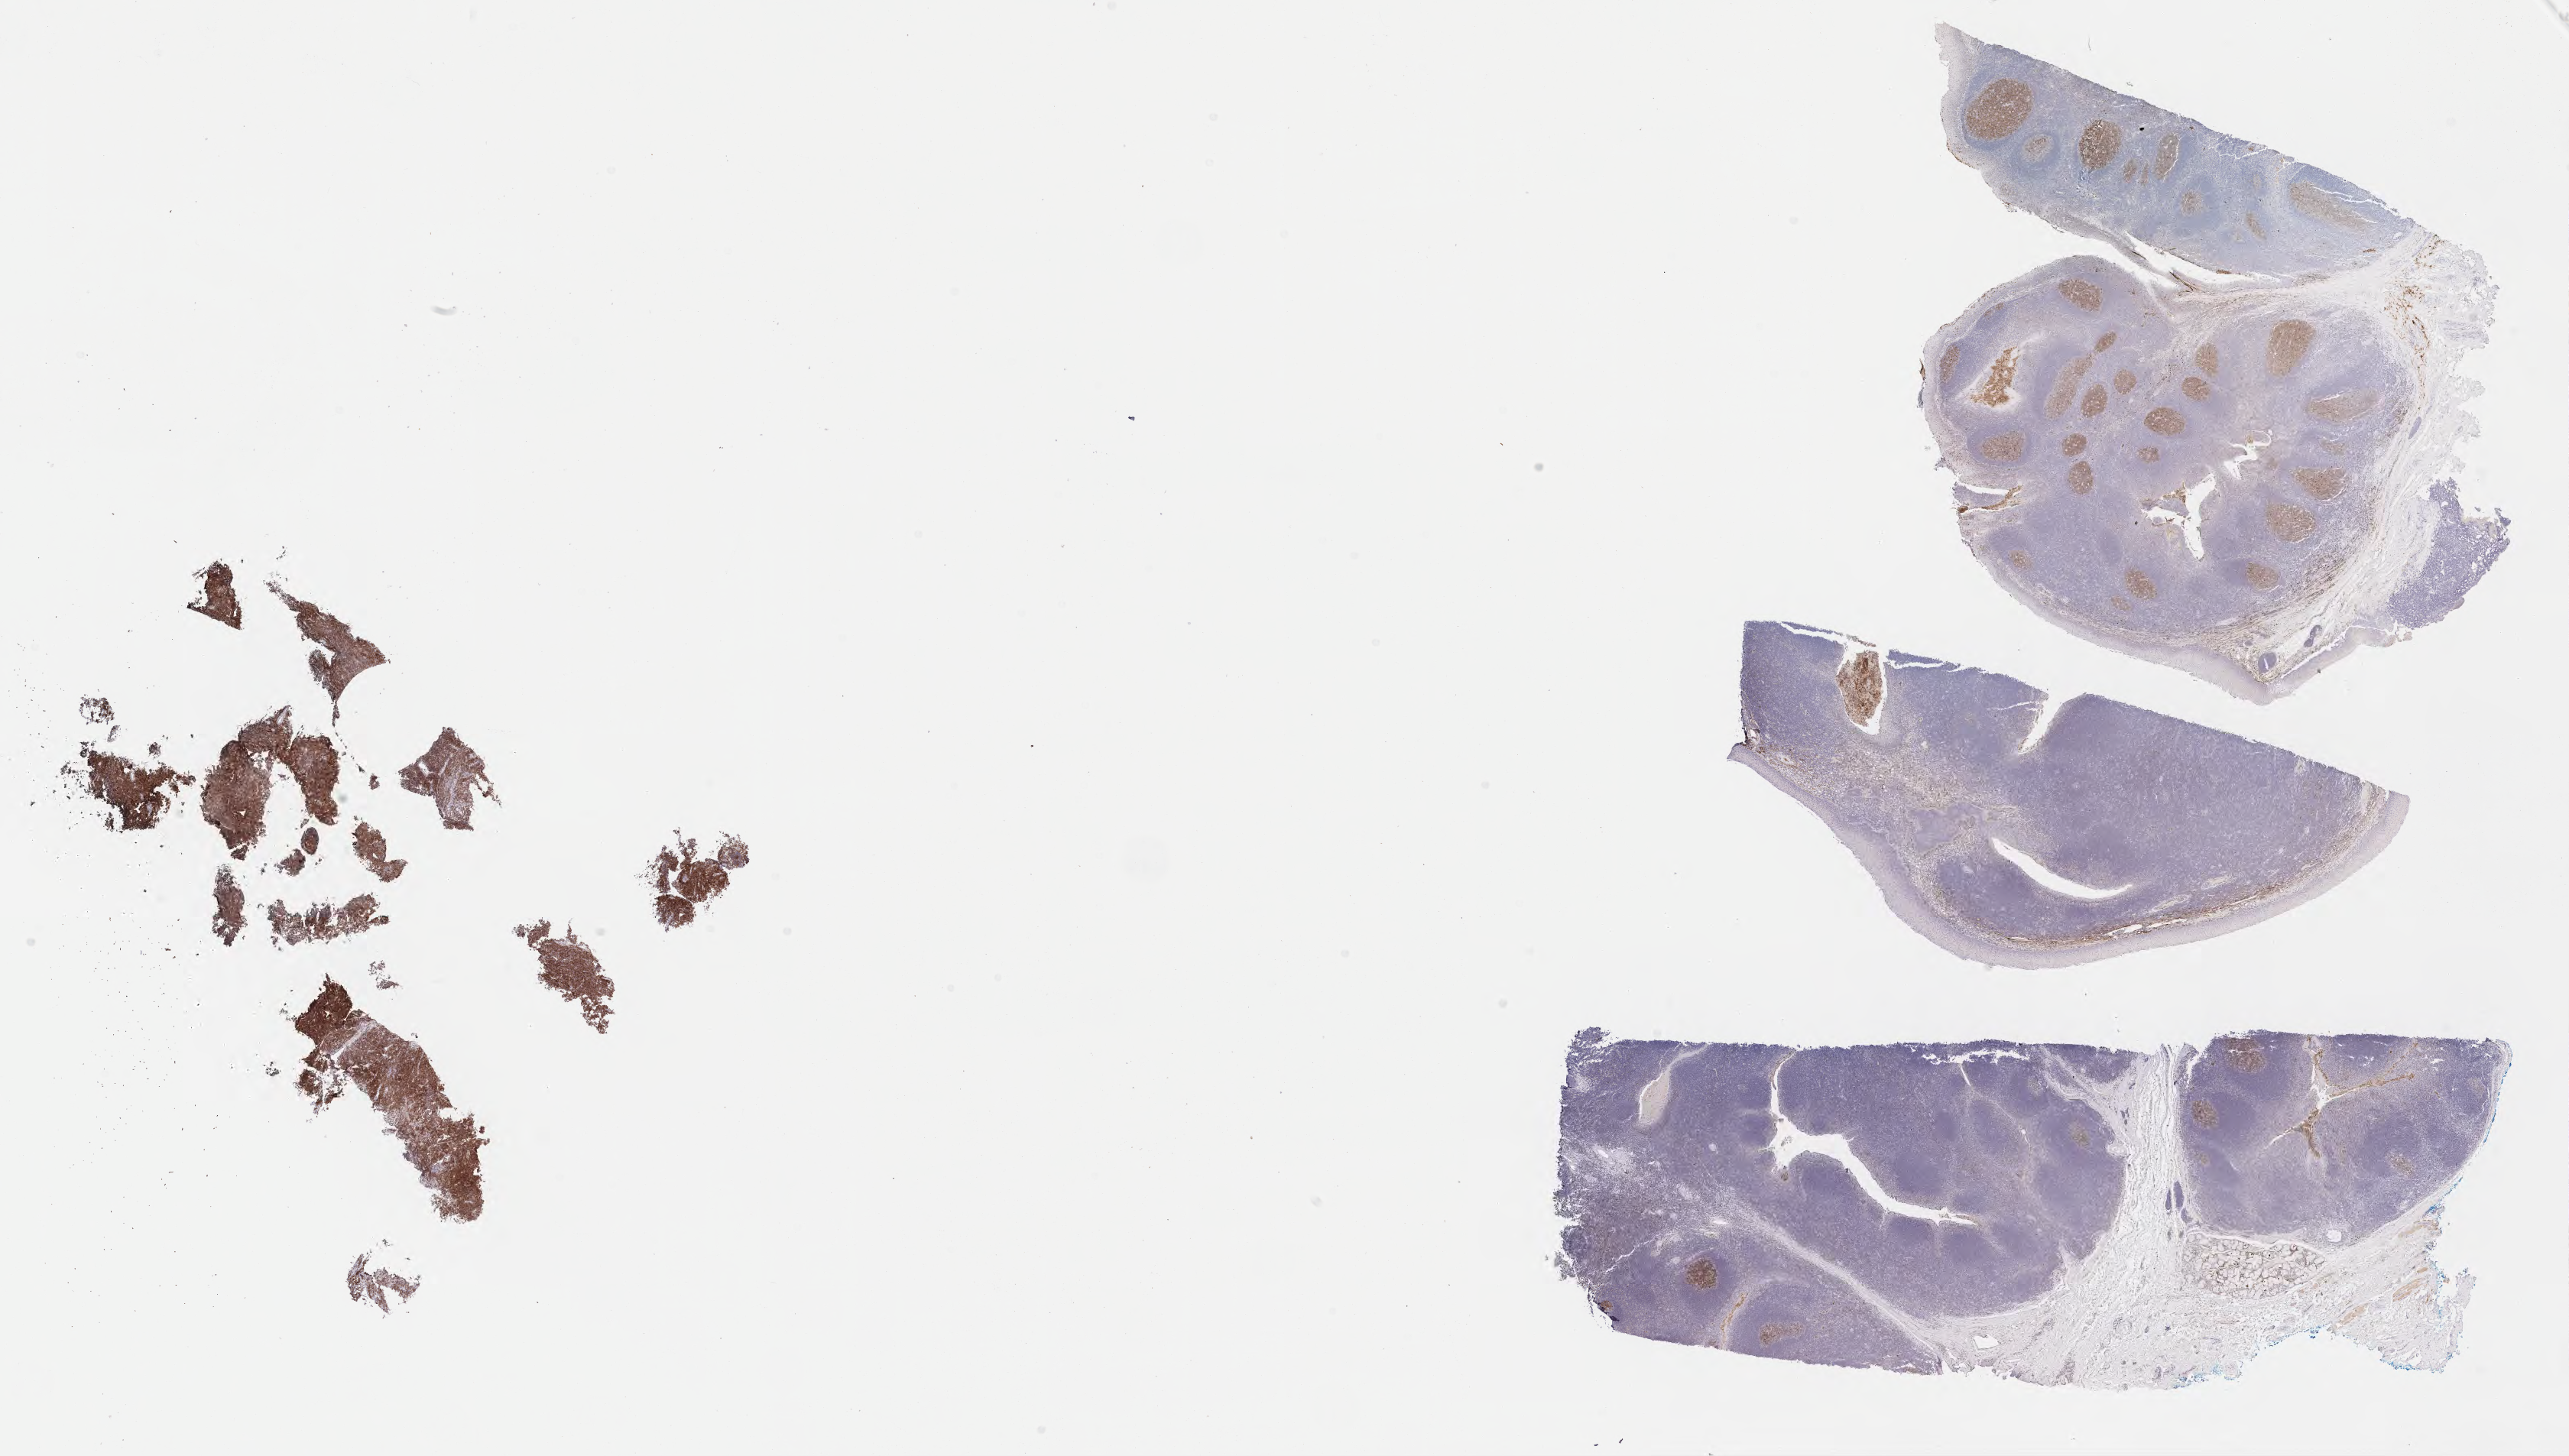
Whole-slide image, immunohistochemical stain for CD10 — shown as a low-resolution overview of the whole scanned area (about 27.2 x 15.4 mm); tumor tissue; site: kidney. Female patient; age at initial diagnosis 8 years.
Histologic diagnosis: Burkitt lymphoma, NOS.